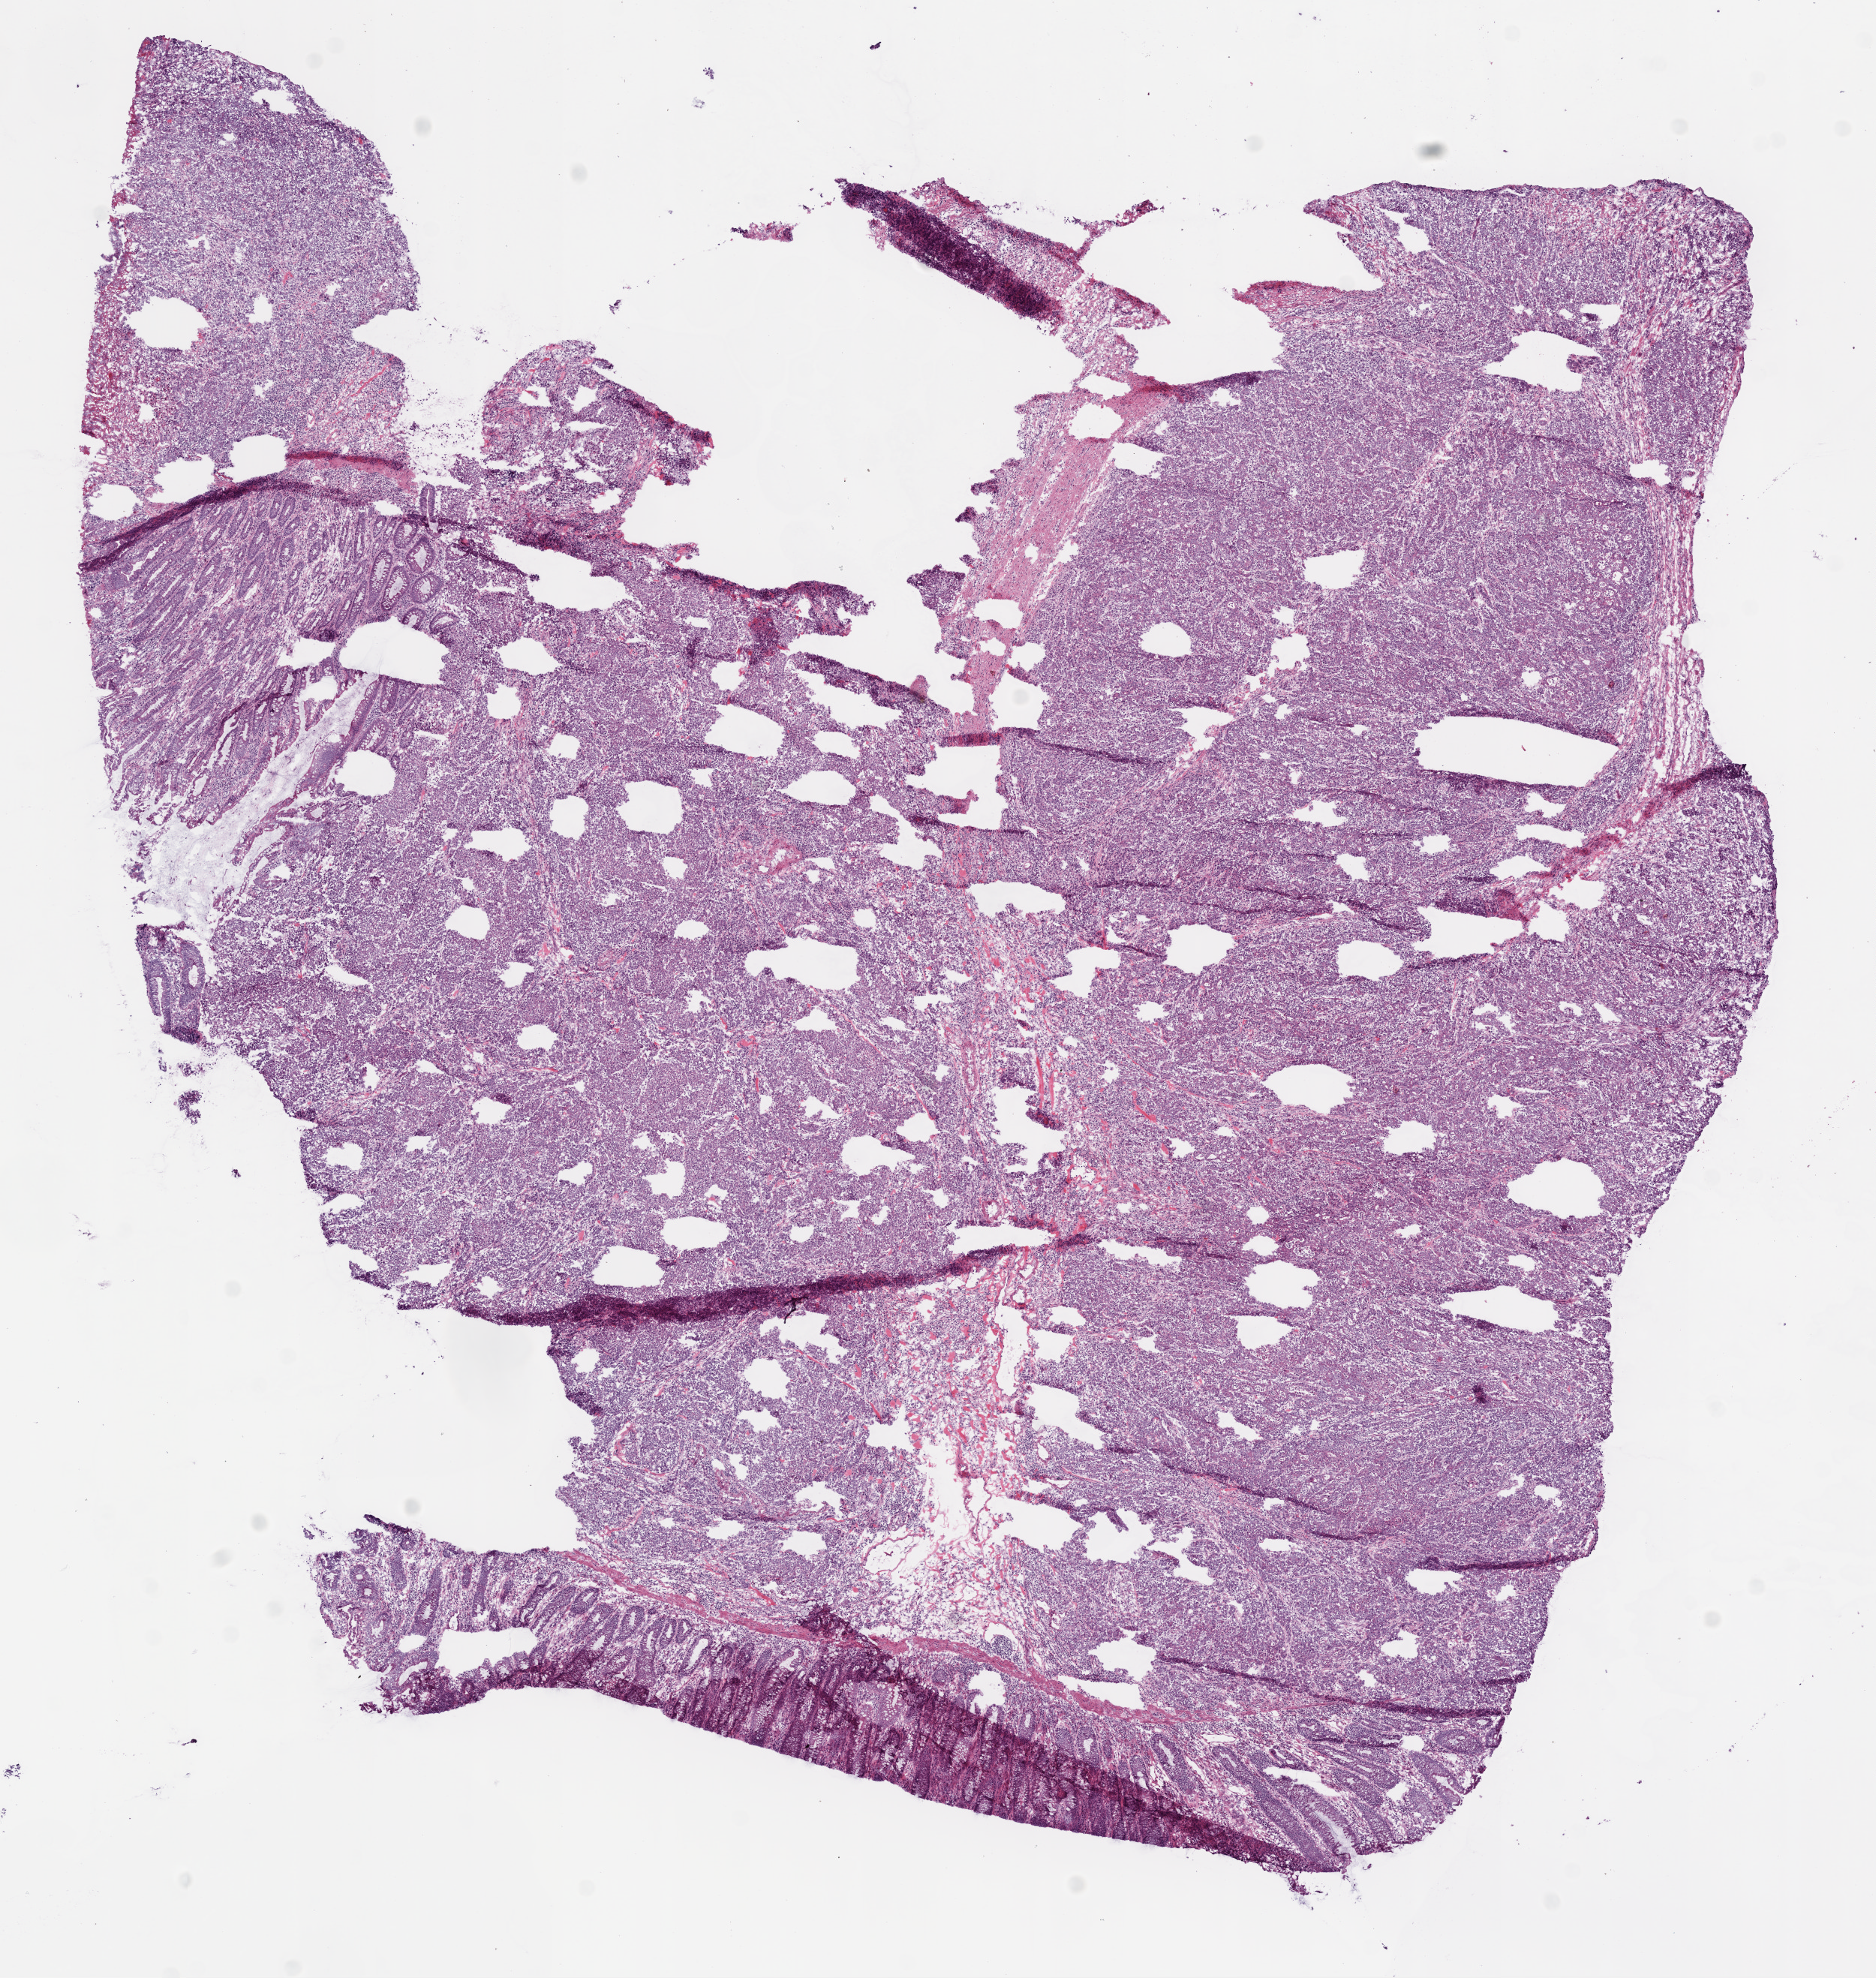
Digitized H&E-stained tissue section (whole slide), whole scanned area (about 10.0 x 10.6 mm, slide scanned at 20x) shown as a low-resolution overview. Frozen section from the bottom of the tissue portion. Sample: primary tumour, colon. Female, age 80 years at initial diagnosis. Composition of this section per pathologist review: tumour cells 90%, tumour nuclei 95%, normal cells 9%, necrosis 1%. Inflammatory infiltration, as recorded: lymphocyte infiltration 2%, neutrophil infiltration 4%.
• histologic diagnosis: Adenocarcinoma, NOS (ascending colon)
• TNM: T3 N0 M0
• lymph nodes positive (case pathology): 0 of 20 examined
• AJCC pathologic stage: IIA